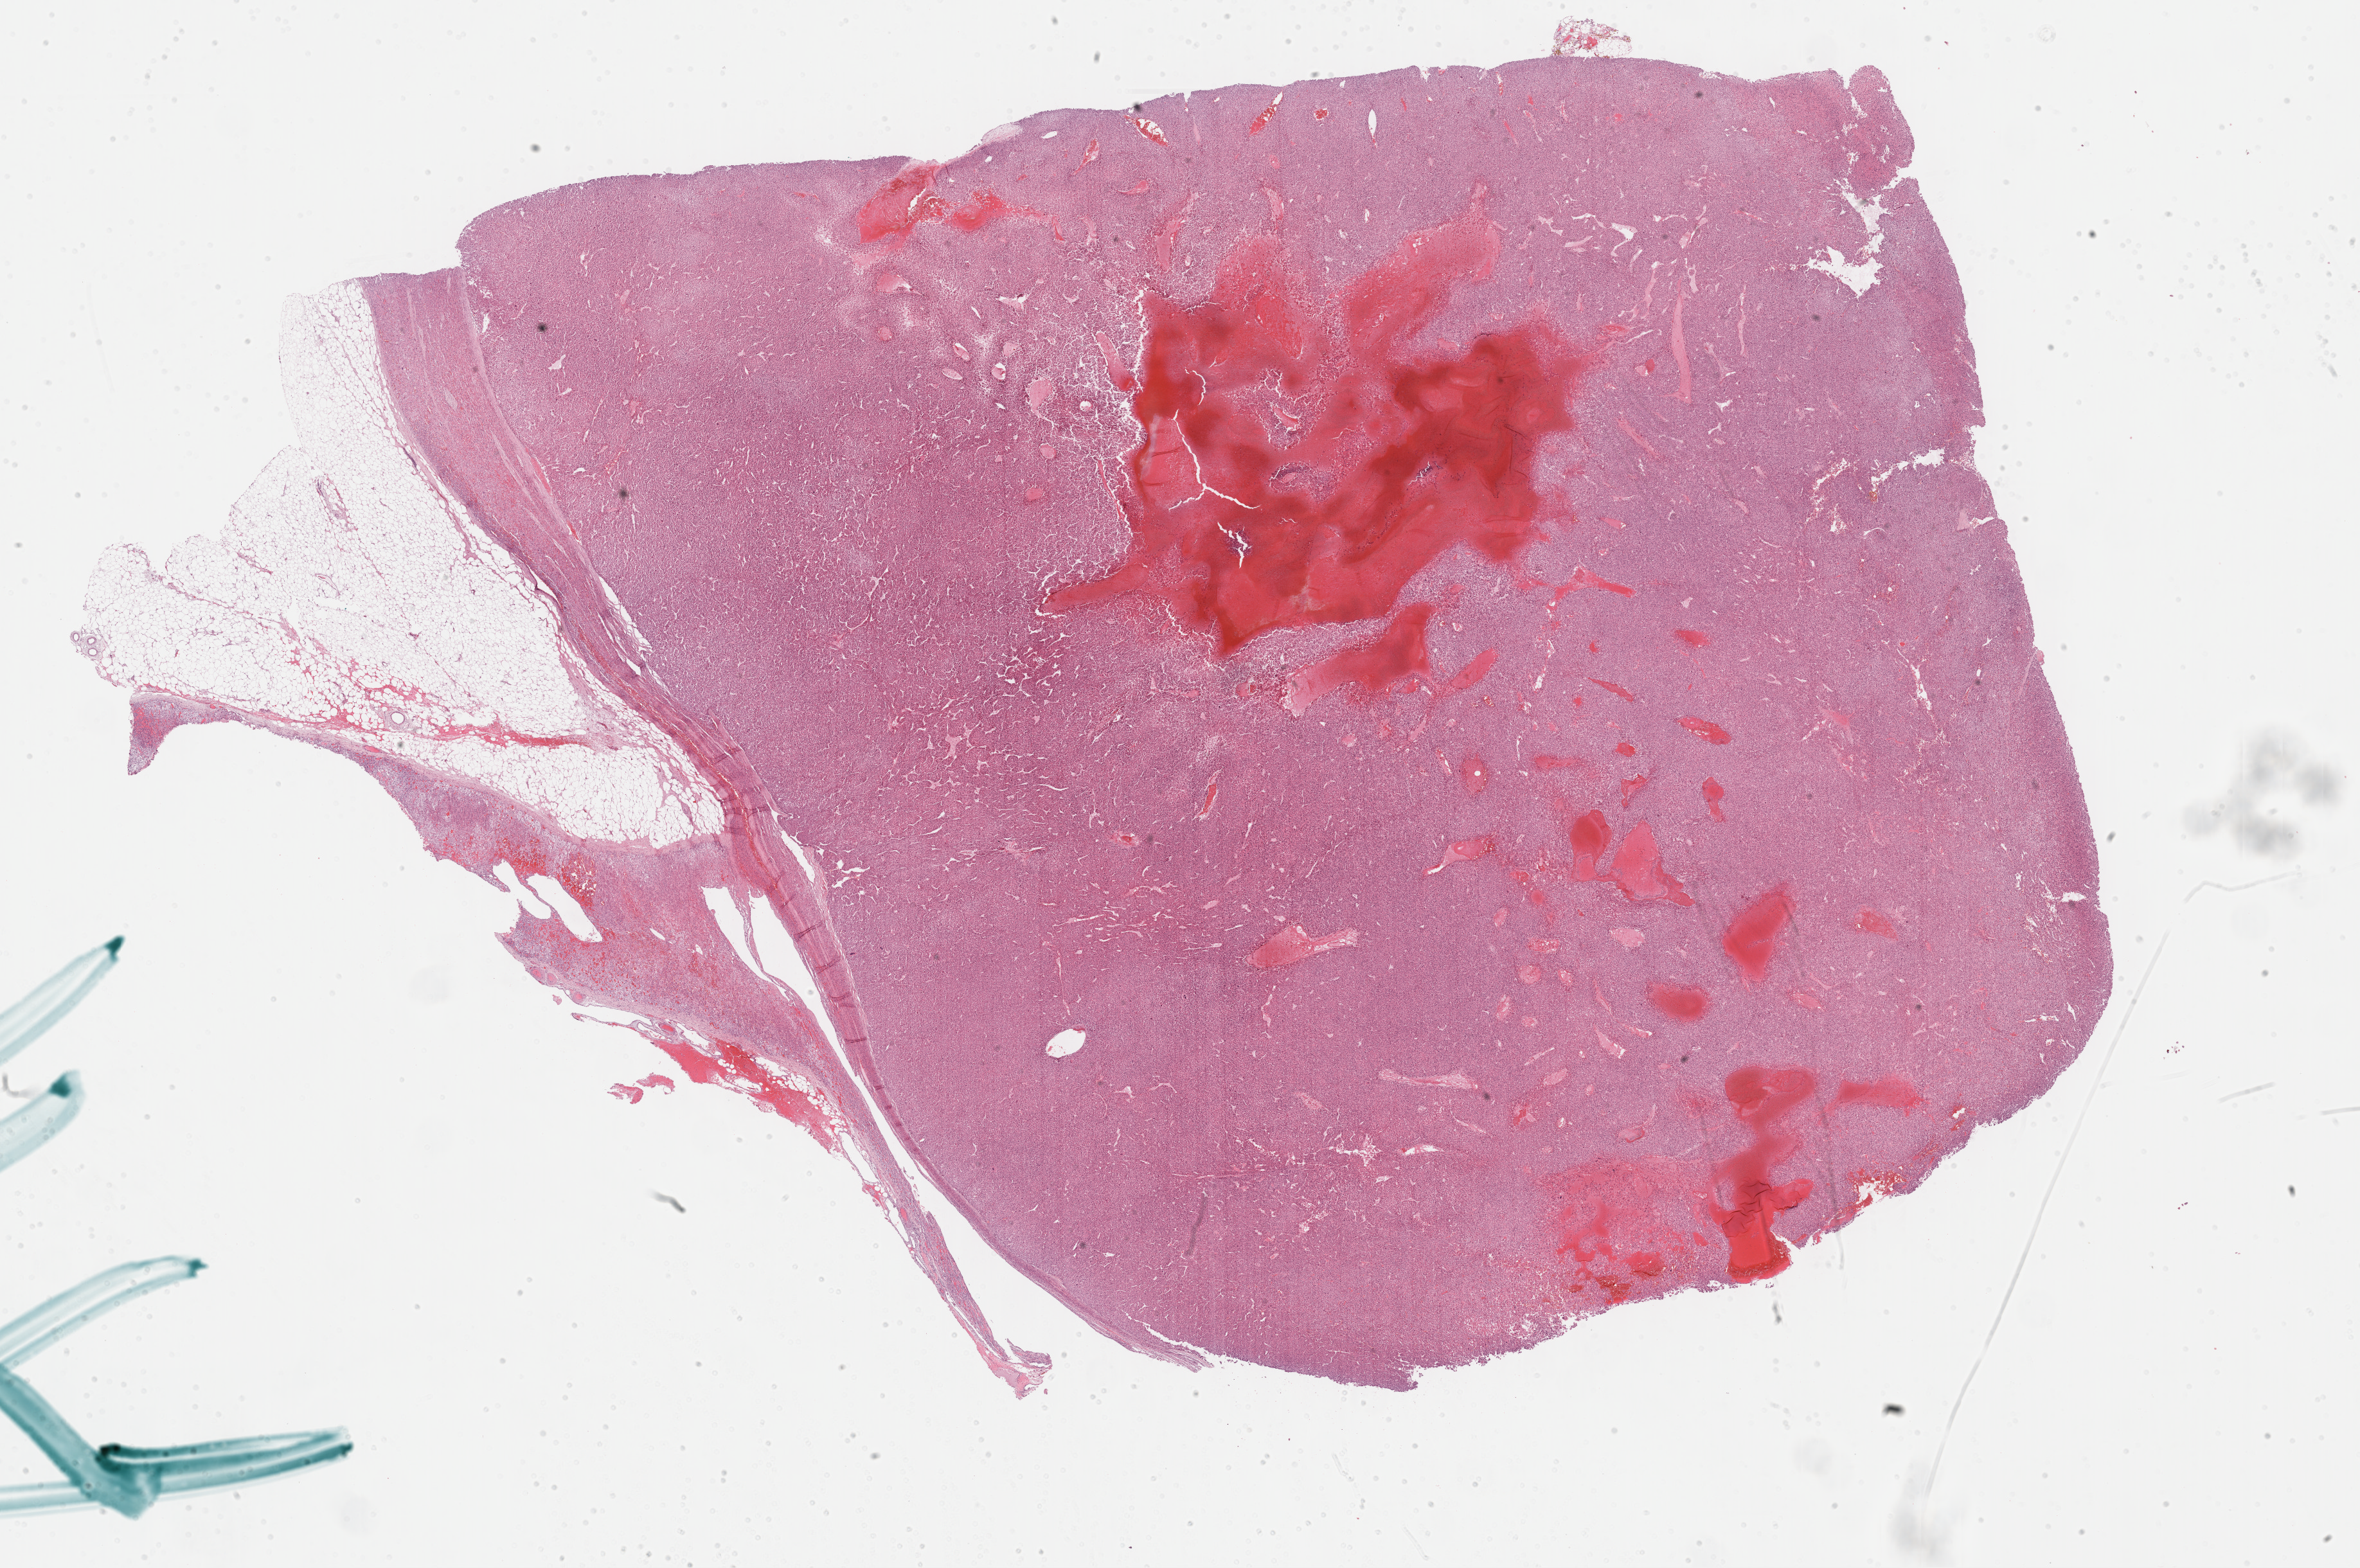
Whole-slide histology image, Hematoxylin and eosin (H&E) stained, low-resolution overview of the scanned area, about 29.7 x 19.7 mm (slide scanned at 40x); formalin-fixed paraffin-embedded (FFPE) diagnostic section; adrenal cortex, primary tumour sample. Patient: male, age at initial diagnosis 60 years.
Laterality: left. Diagnosis: Adrenal cortical carcinoma (cortex of adrenal gland).